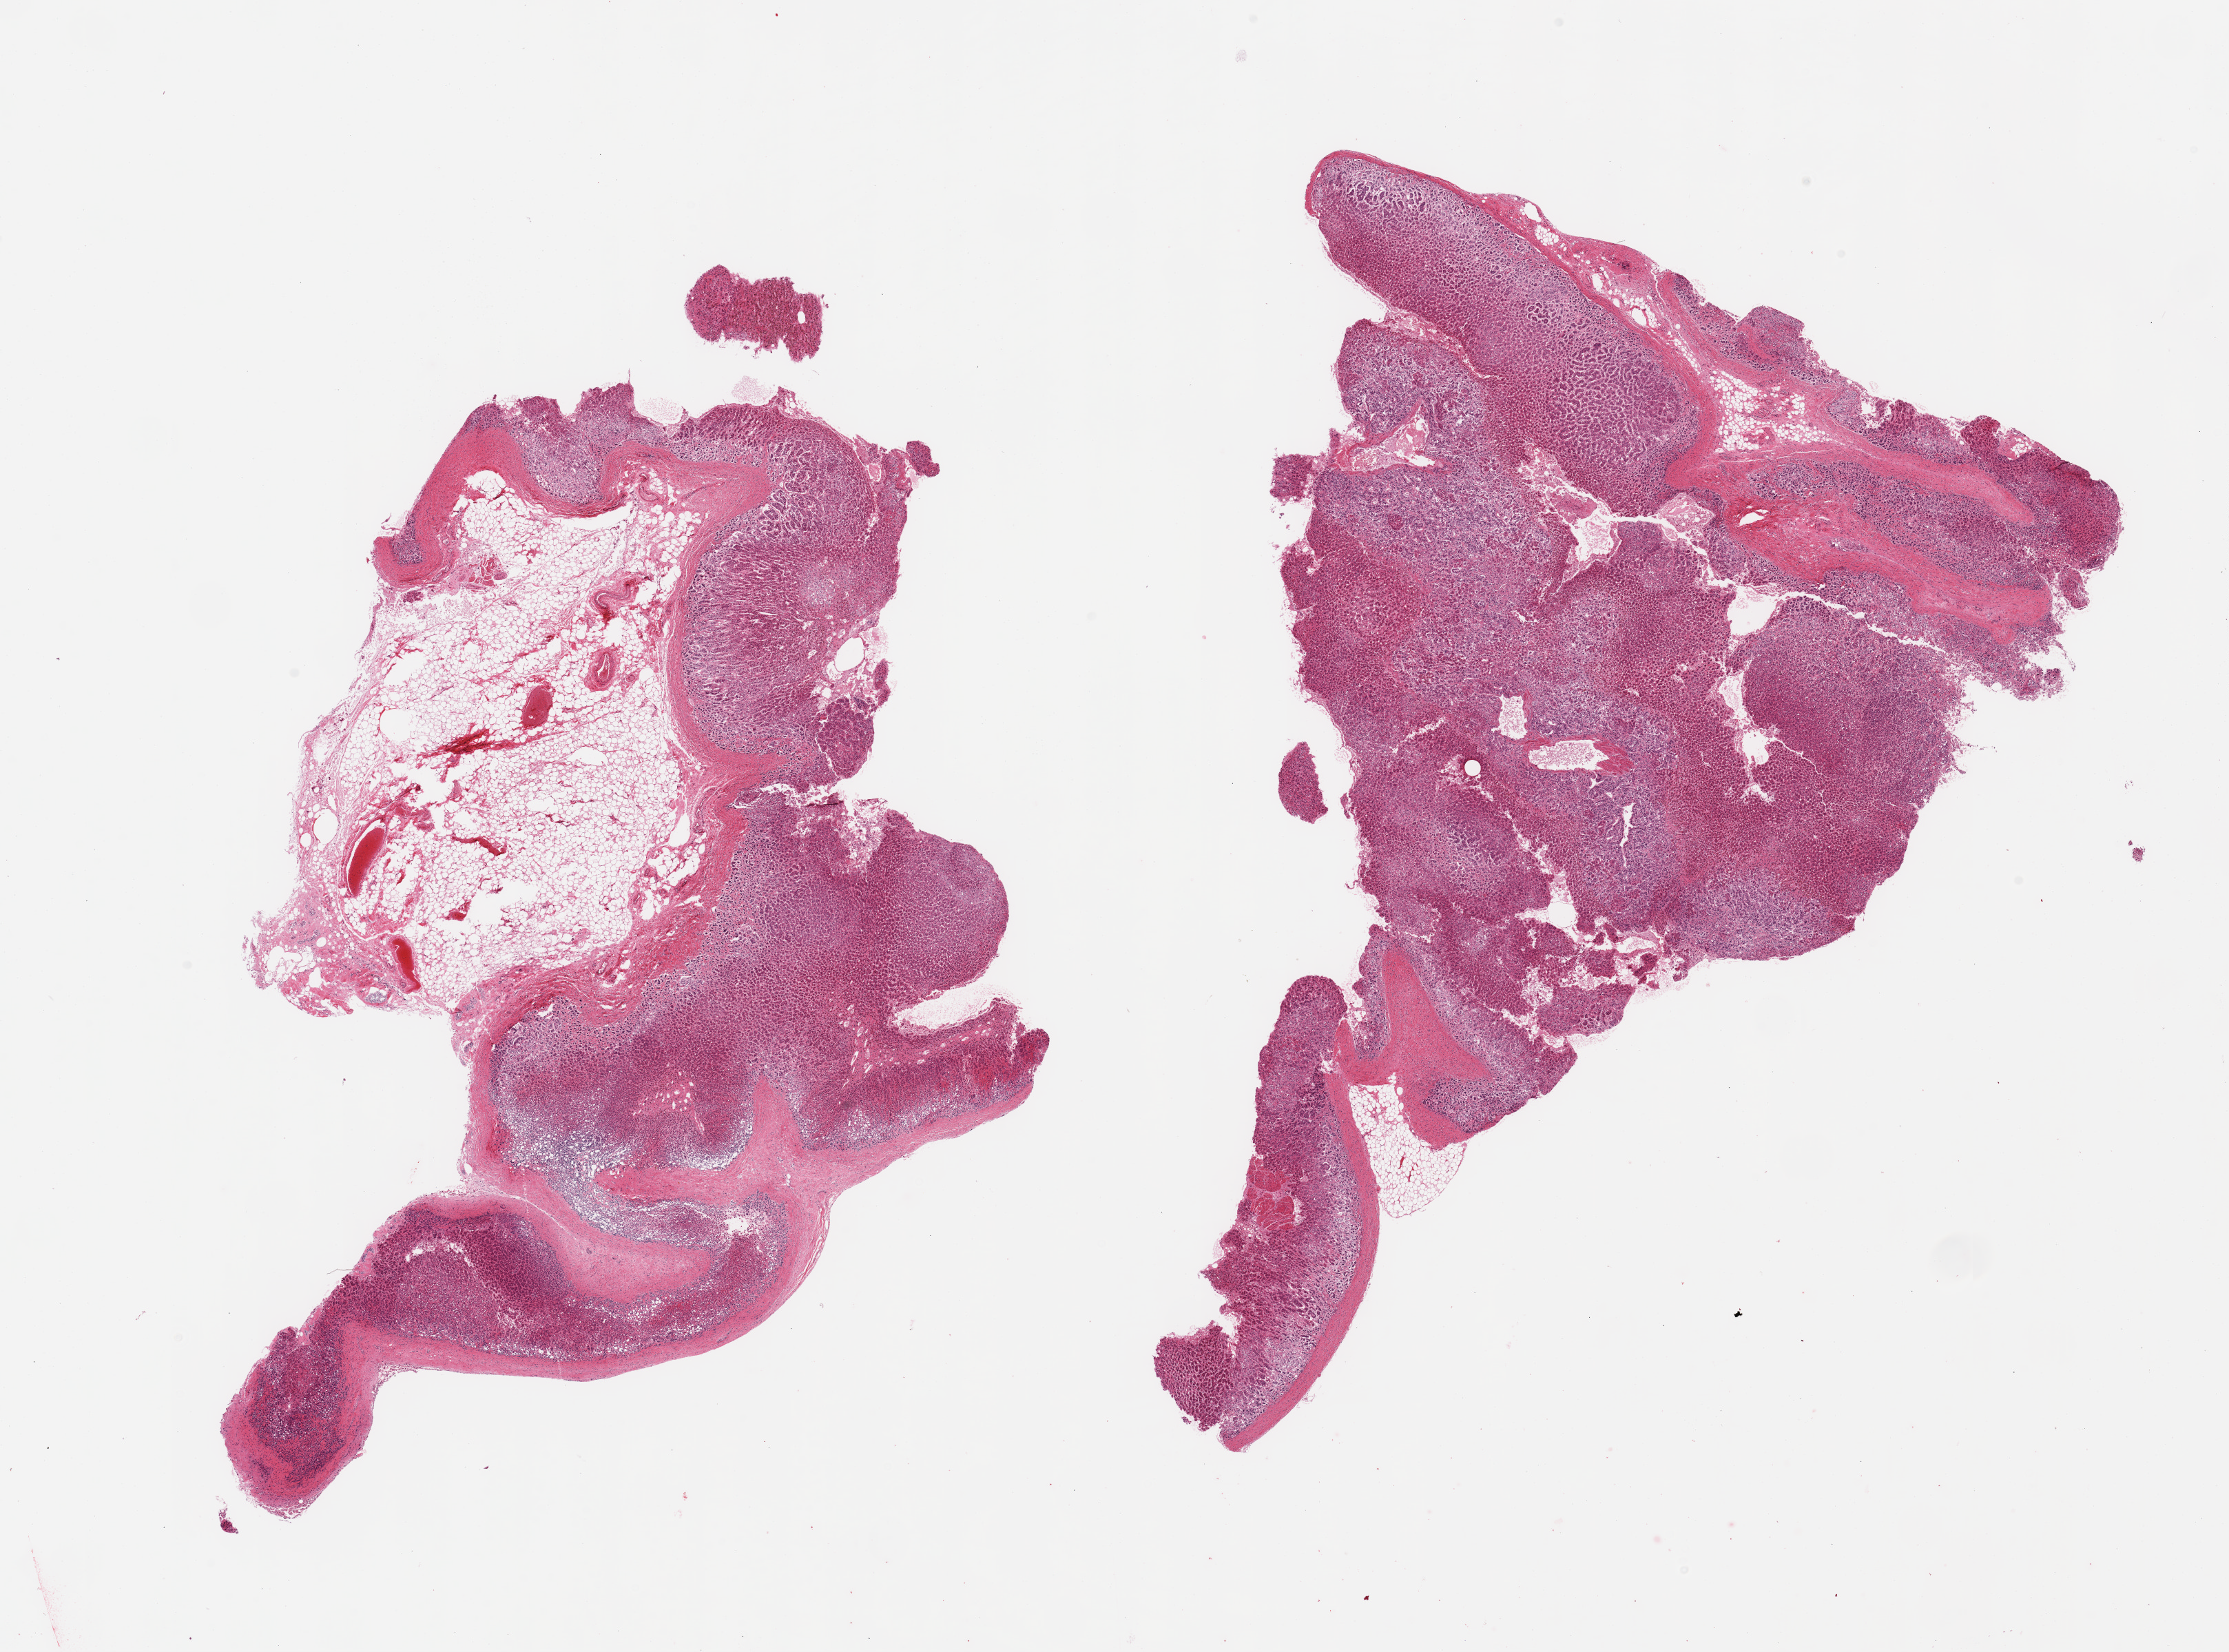
Digitized hematoxylin and eosin (H&E)-stained section — low-resolution overview of the scanned area, about 25.6 x 19.0 mm, PAXgene-fixed, paraffin-embedded tissue, section of adrenal gland (target tissue), donor tissue sample. Donor: female.
Pathologist's review note for this sample: 2 pieces; 1 piece includes ~30% attached fat.